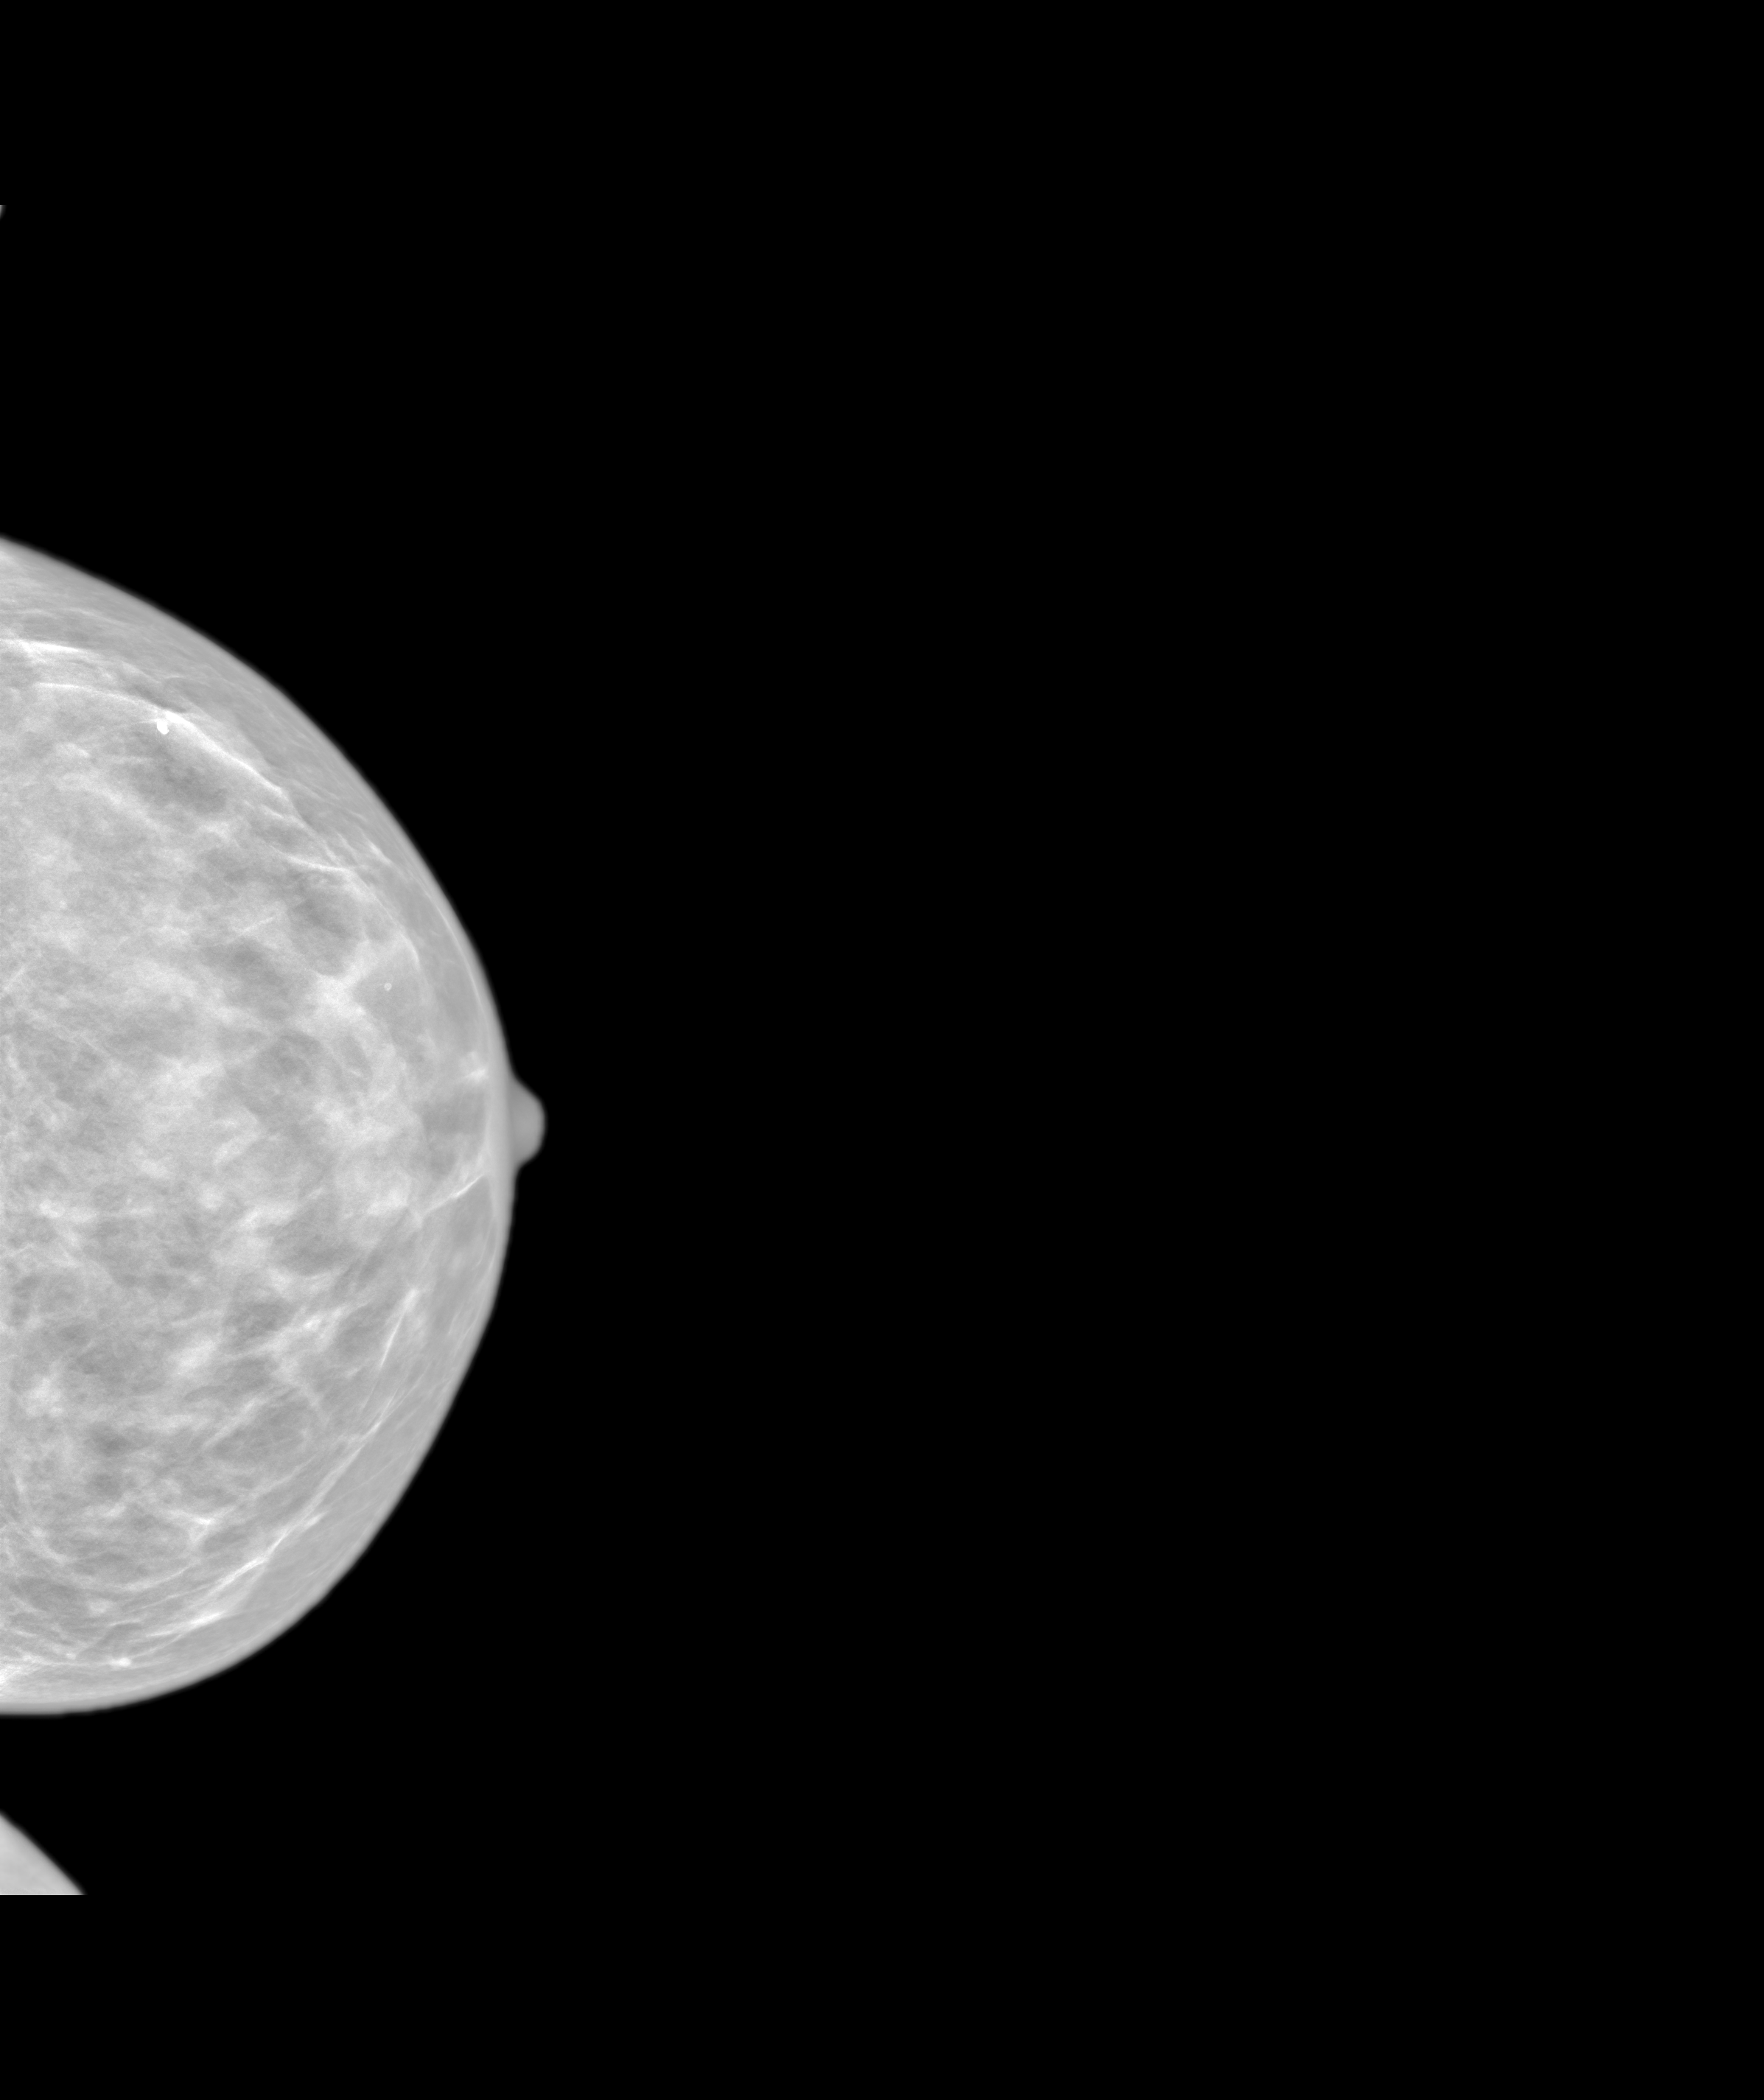
Screening examination. Patient aged 44 years (female).
Image type: synthesized 2-D view from tomosynthesis. Breast: left. Projection: craniocaudal (CC) view.